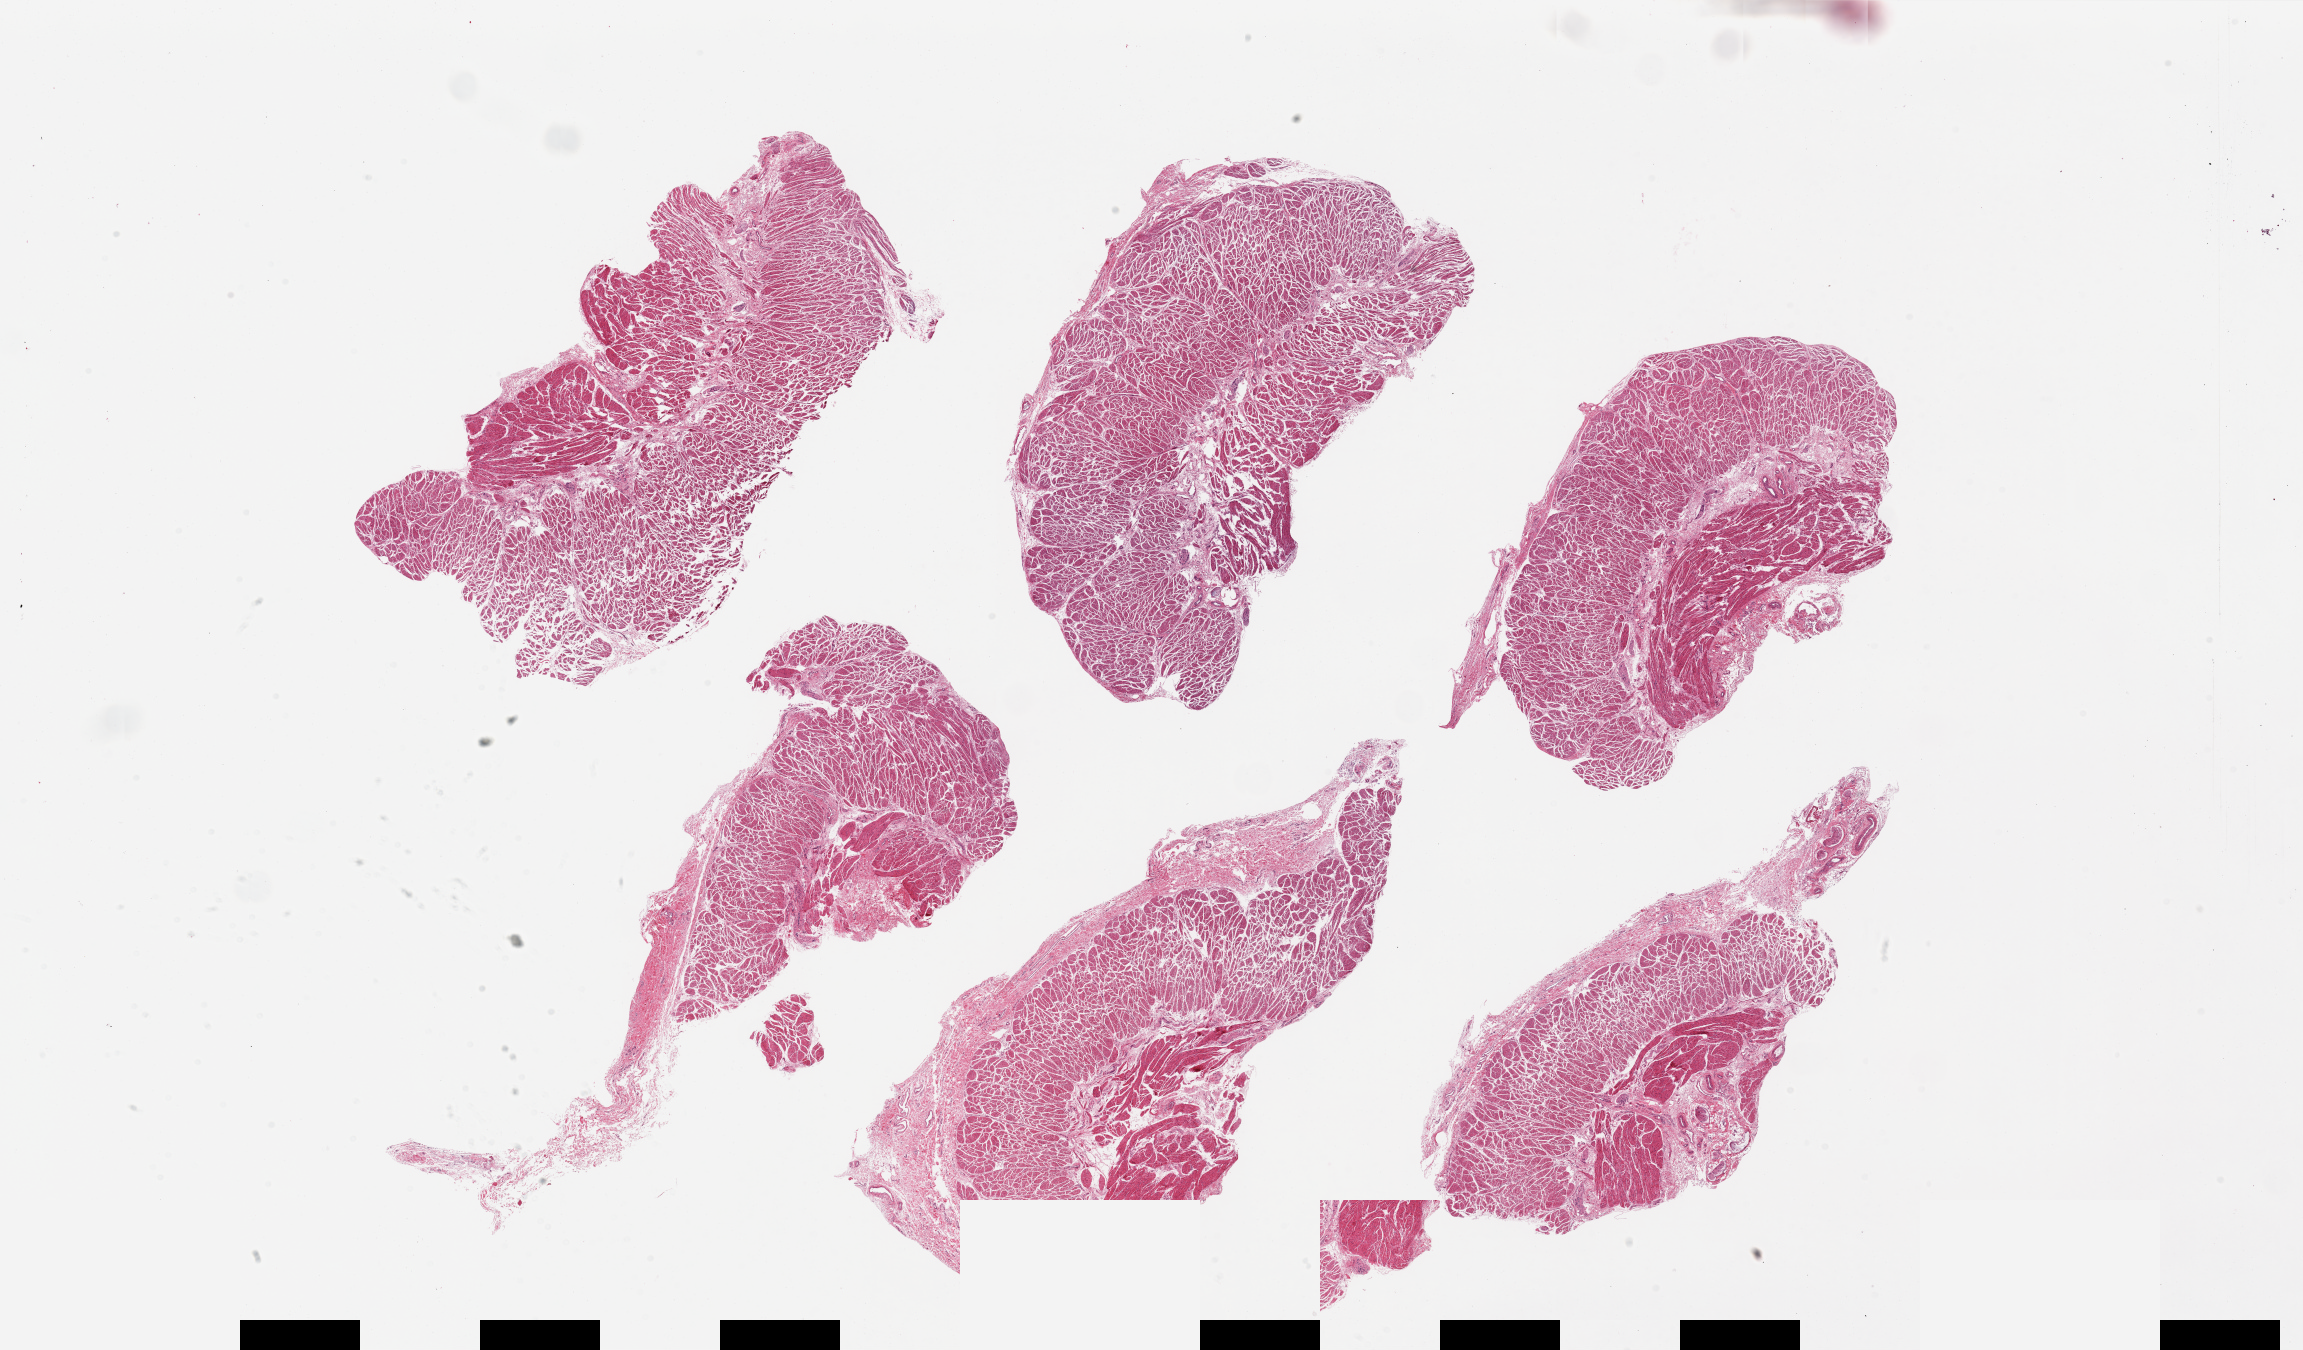
Whole-slide image, H&E stain, brightfield, shown as a low-resolution overview of the whole scanned area (about 36.4 x 21.4 mm, from a 20x scan), PAXgene-fixed paraffin-embedded (PFPE) section, target tissue: gastroesophageal junction, tissue donor sample. Female donor.
* pathologist's review note for this sample: 6 pieces. up to 12x6mm; Most well dissected; some periesophageal stroma